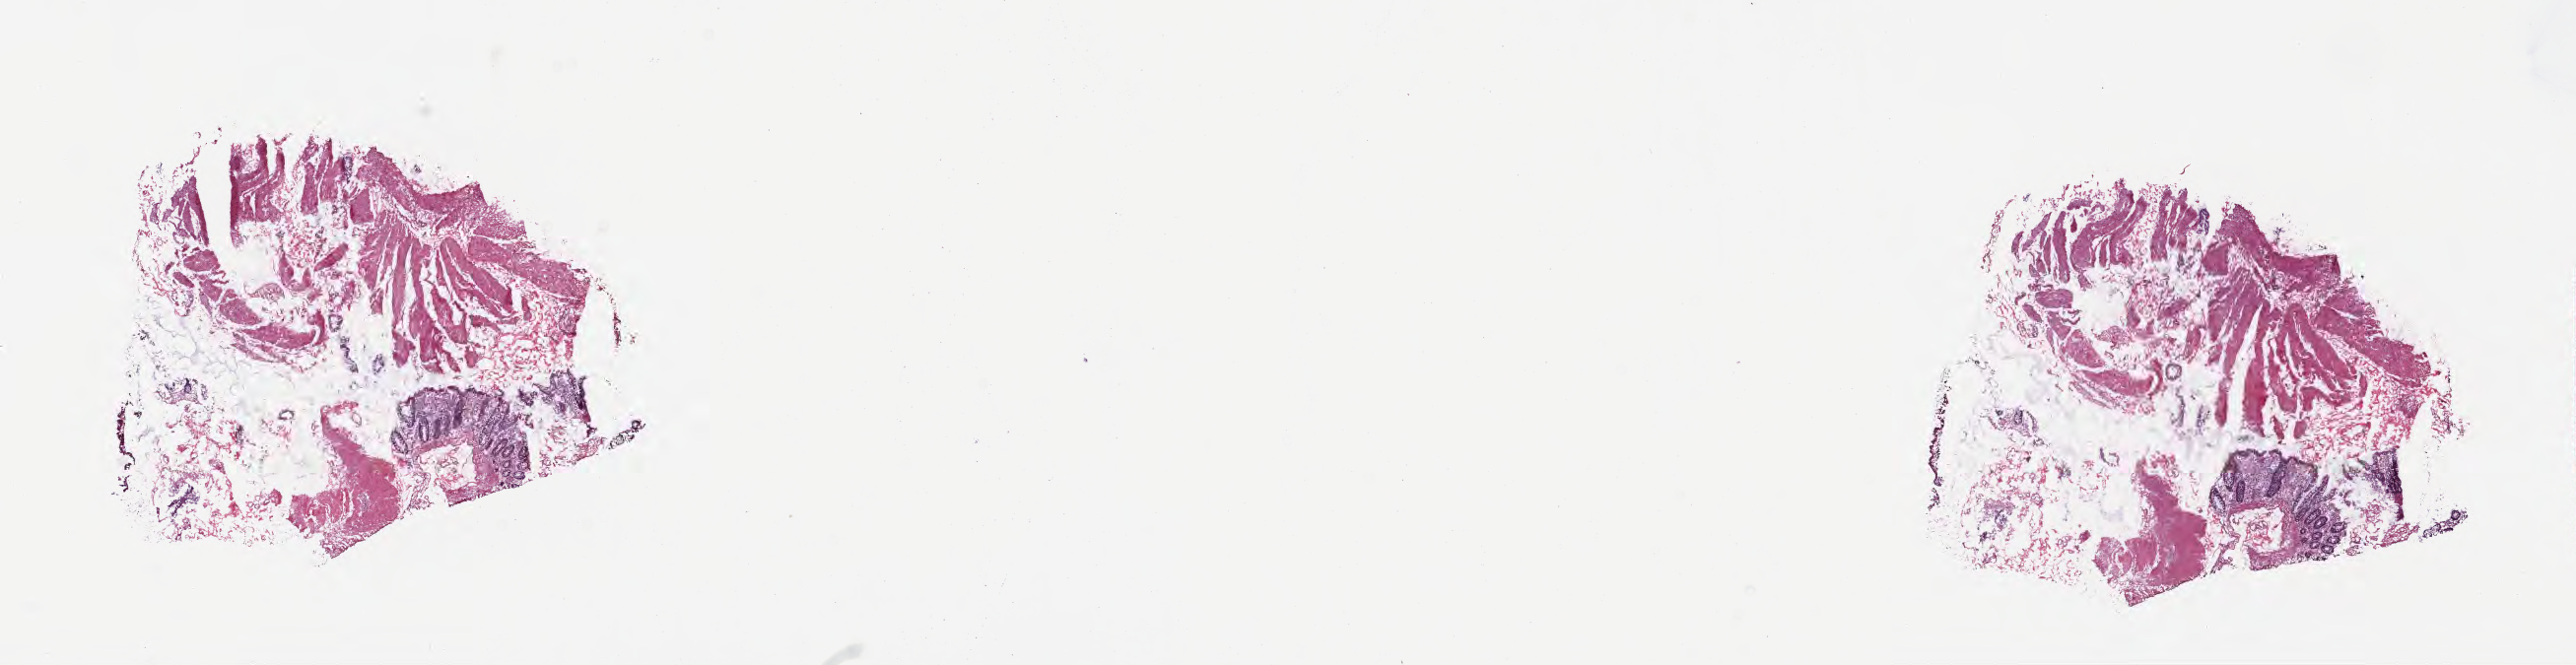
H&E whole-slide image, shown as a low-resolution overview of the whole scanned area (about 21.1 x 5.5 mm). Cryosection. Specimen: non-tumor (normal tissue) sample from a patient with adenocarcinoma, NOS. Anatomic site: cecum. Male, age 74 years at initial diagnosis. Pathologist review of this section (percent, as recorded): tumor cells 0%, tumor nuclei 0%, stromal cells 85%, necrosis 0%, normal cells 15%. Infiltration values recorded for this section: lymphocyte infiltration 65%, monocyte infiltration 1%, neutrophil infiltration 0%.
This section: non-tumor tissue sample; the patient's diagnosis is given above. Section: bottom of the tissue portion.